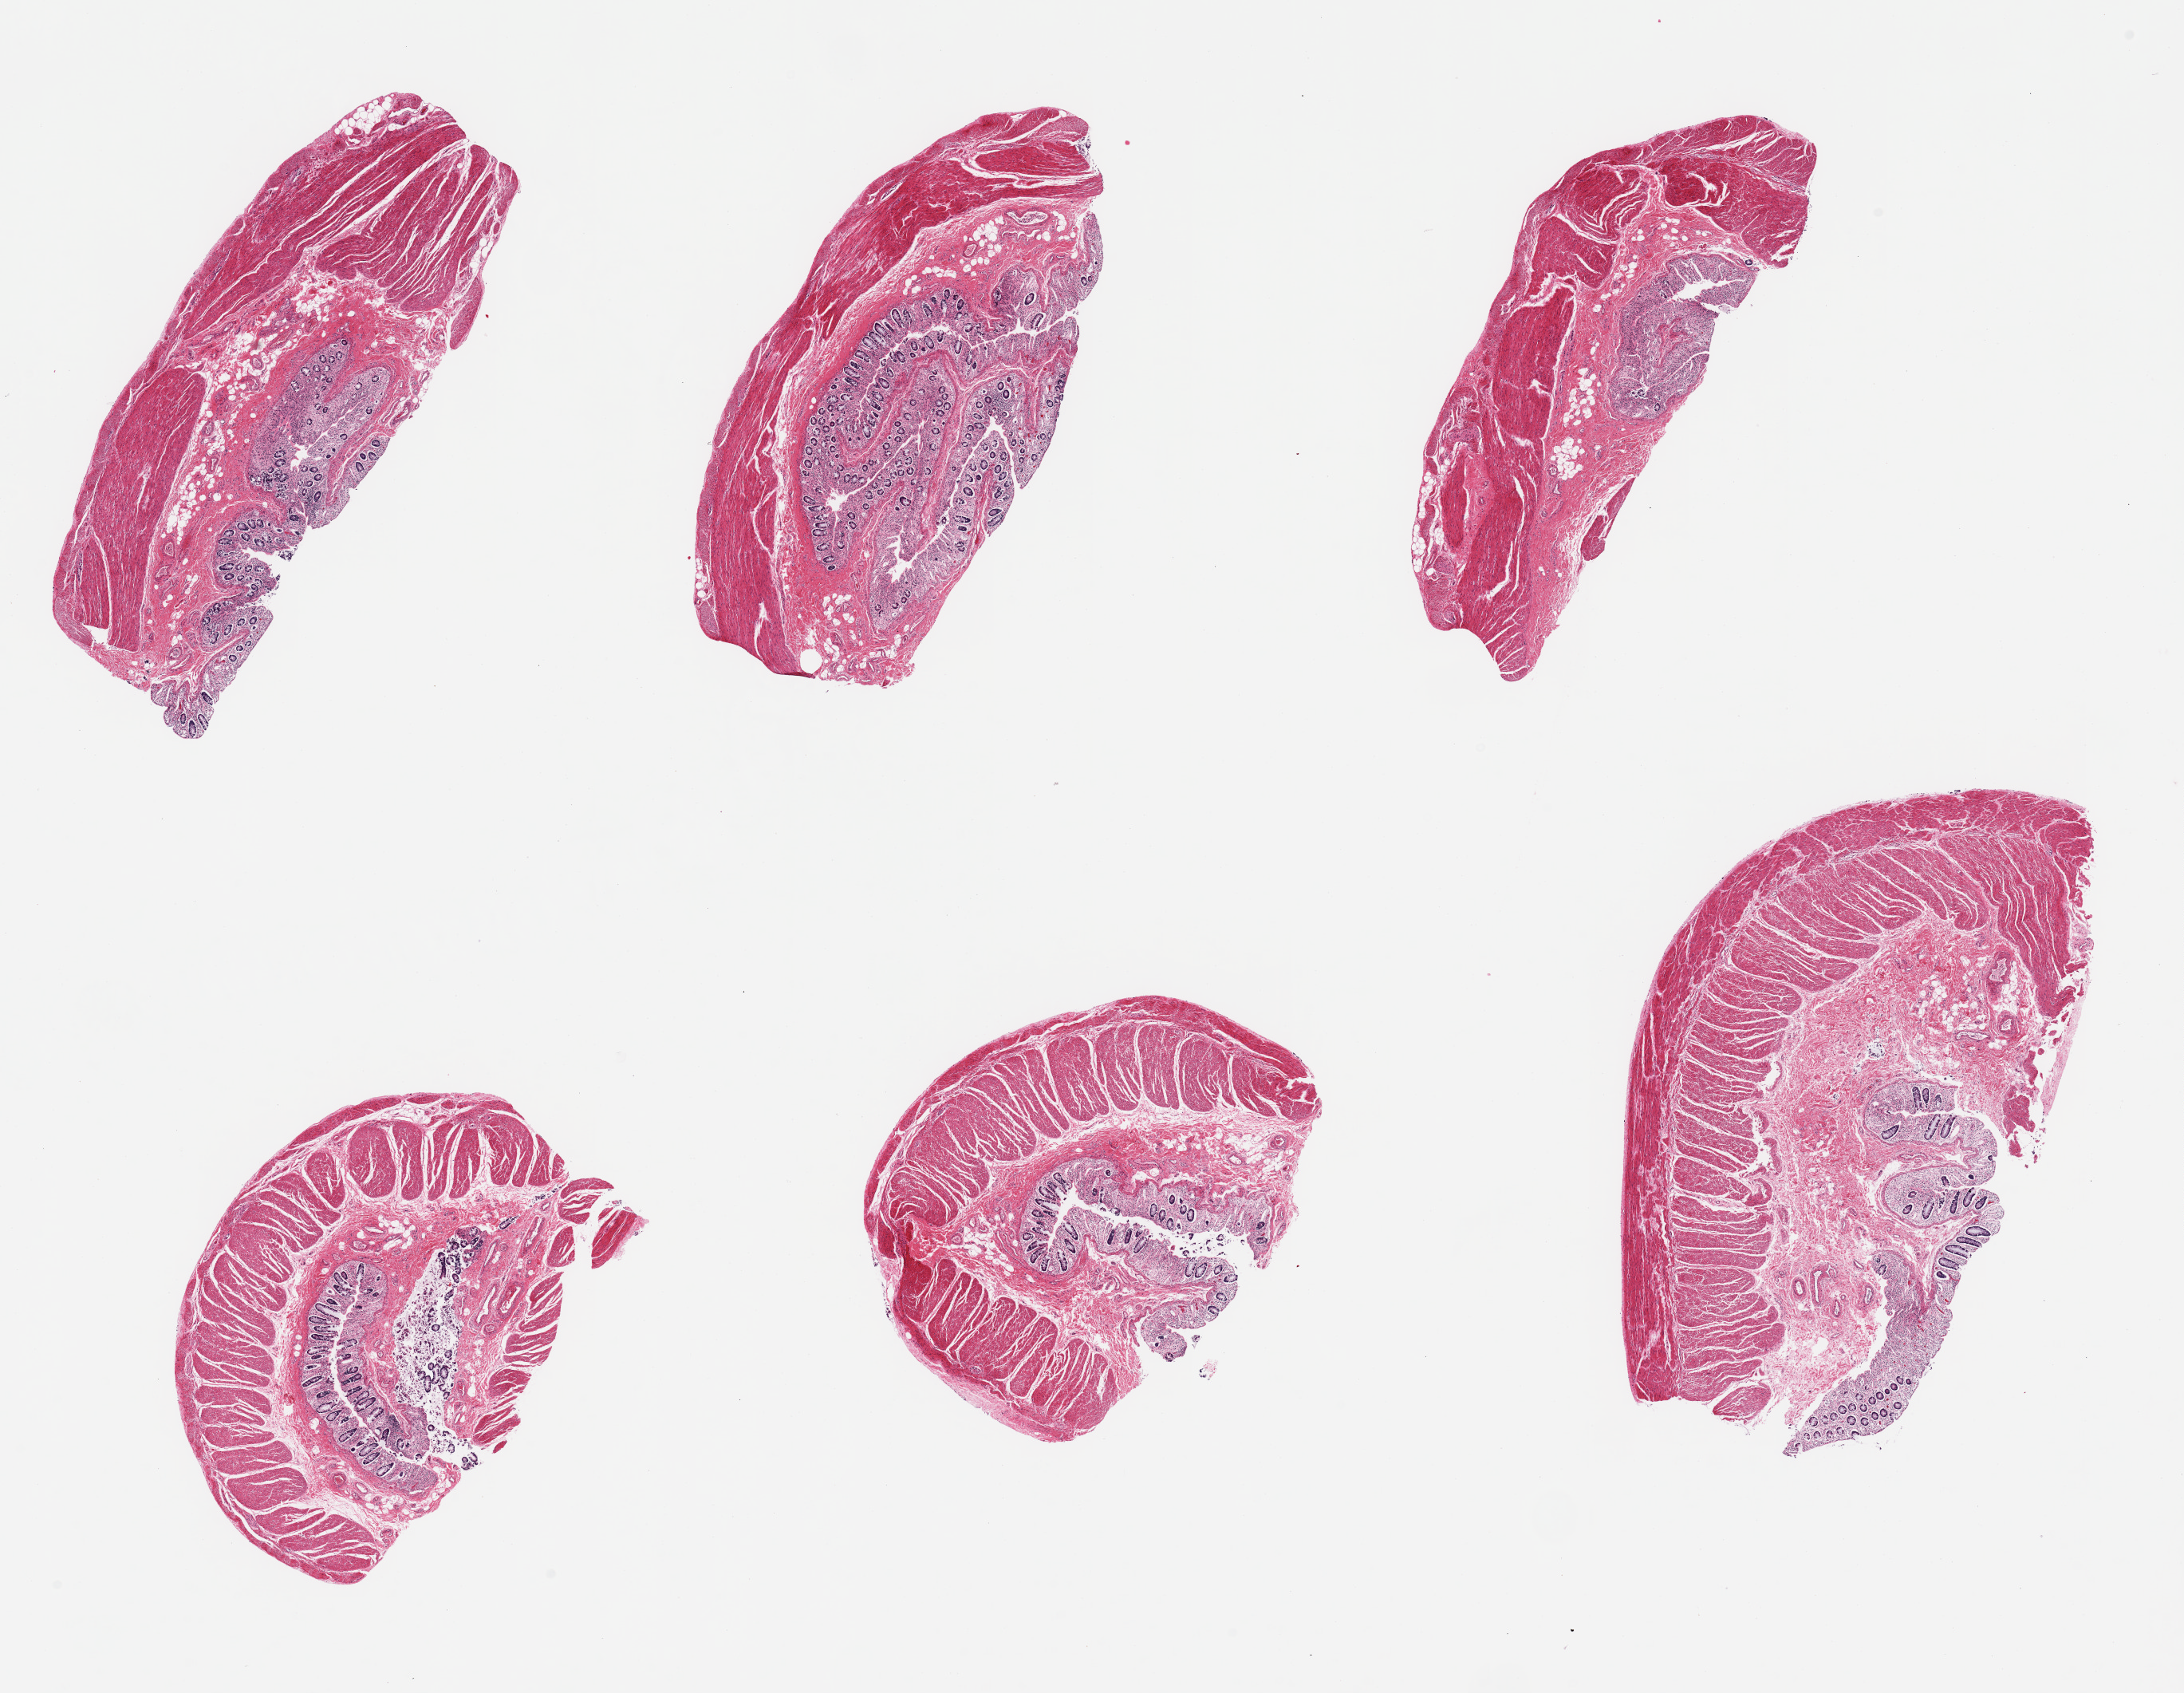
Haematoxylin and eosin whole-slide image, brightfield — shown as a low-resolution overview of the whole scanned area (about 21.7 x 16.8 mm); PAXgene-fixed, paraffin-embedded tissue; section of sigmoid colon (target tissue); tissue donor sample. Female donor.
Reviewer comment on this tissue sample: 6 pieces; all have mucosa as well as muscularis.